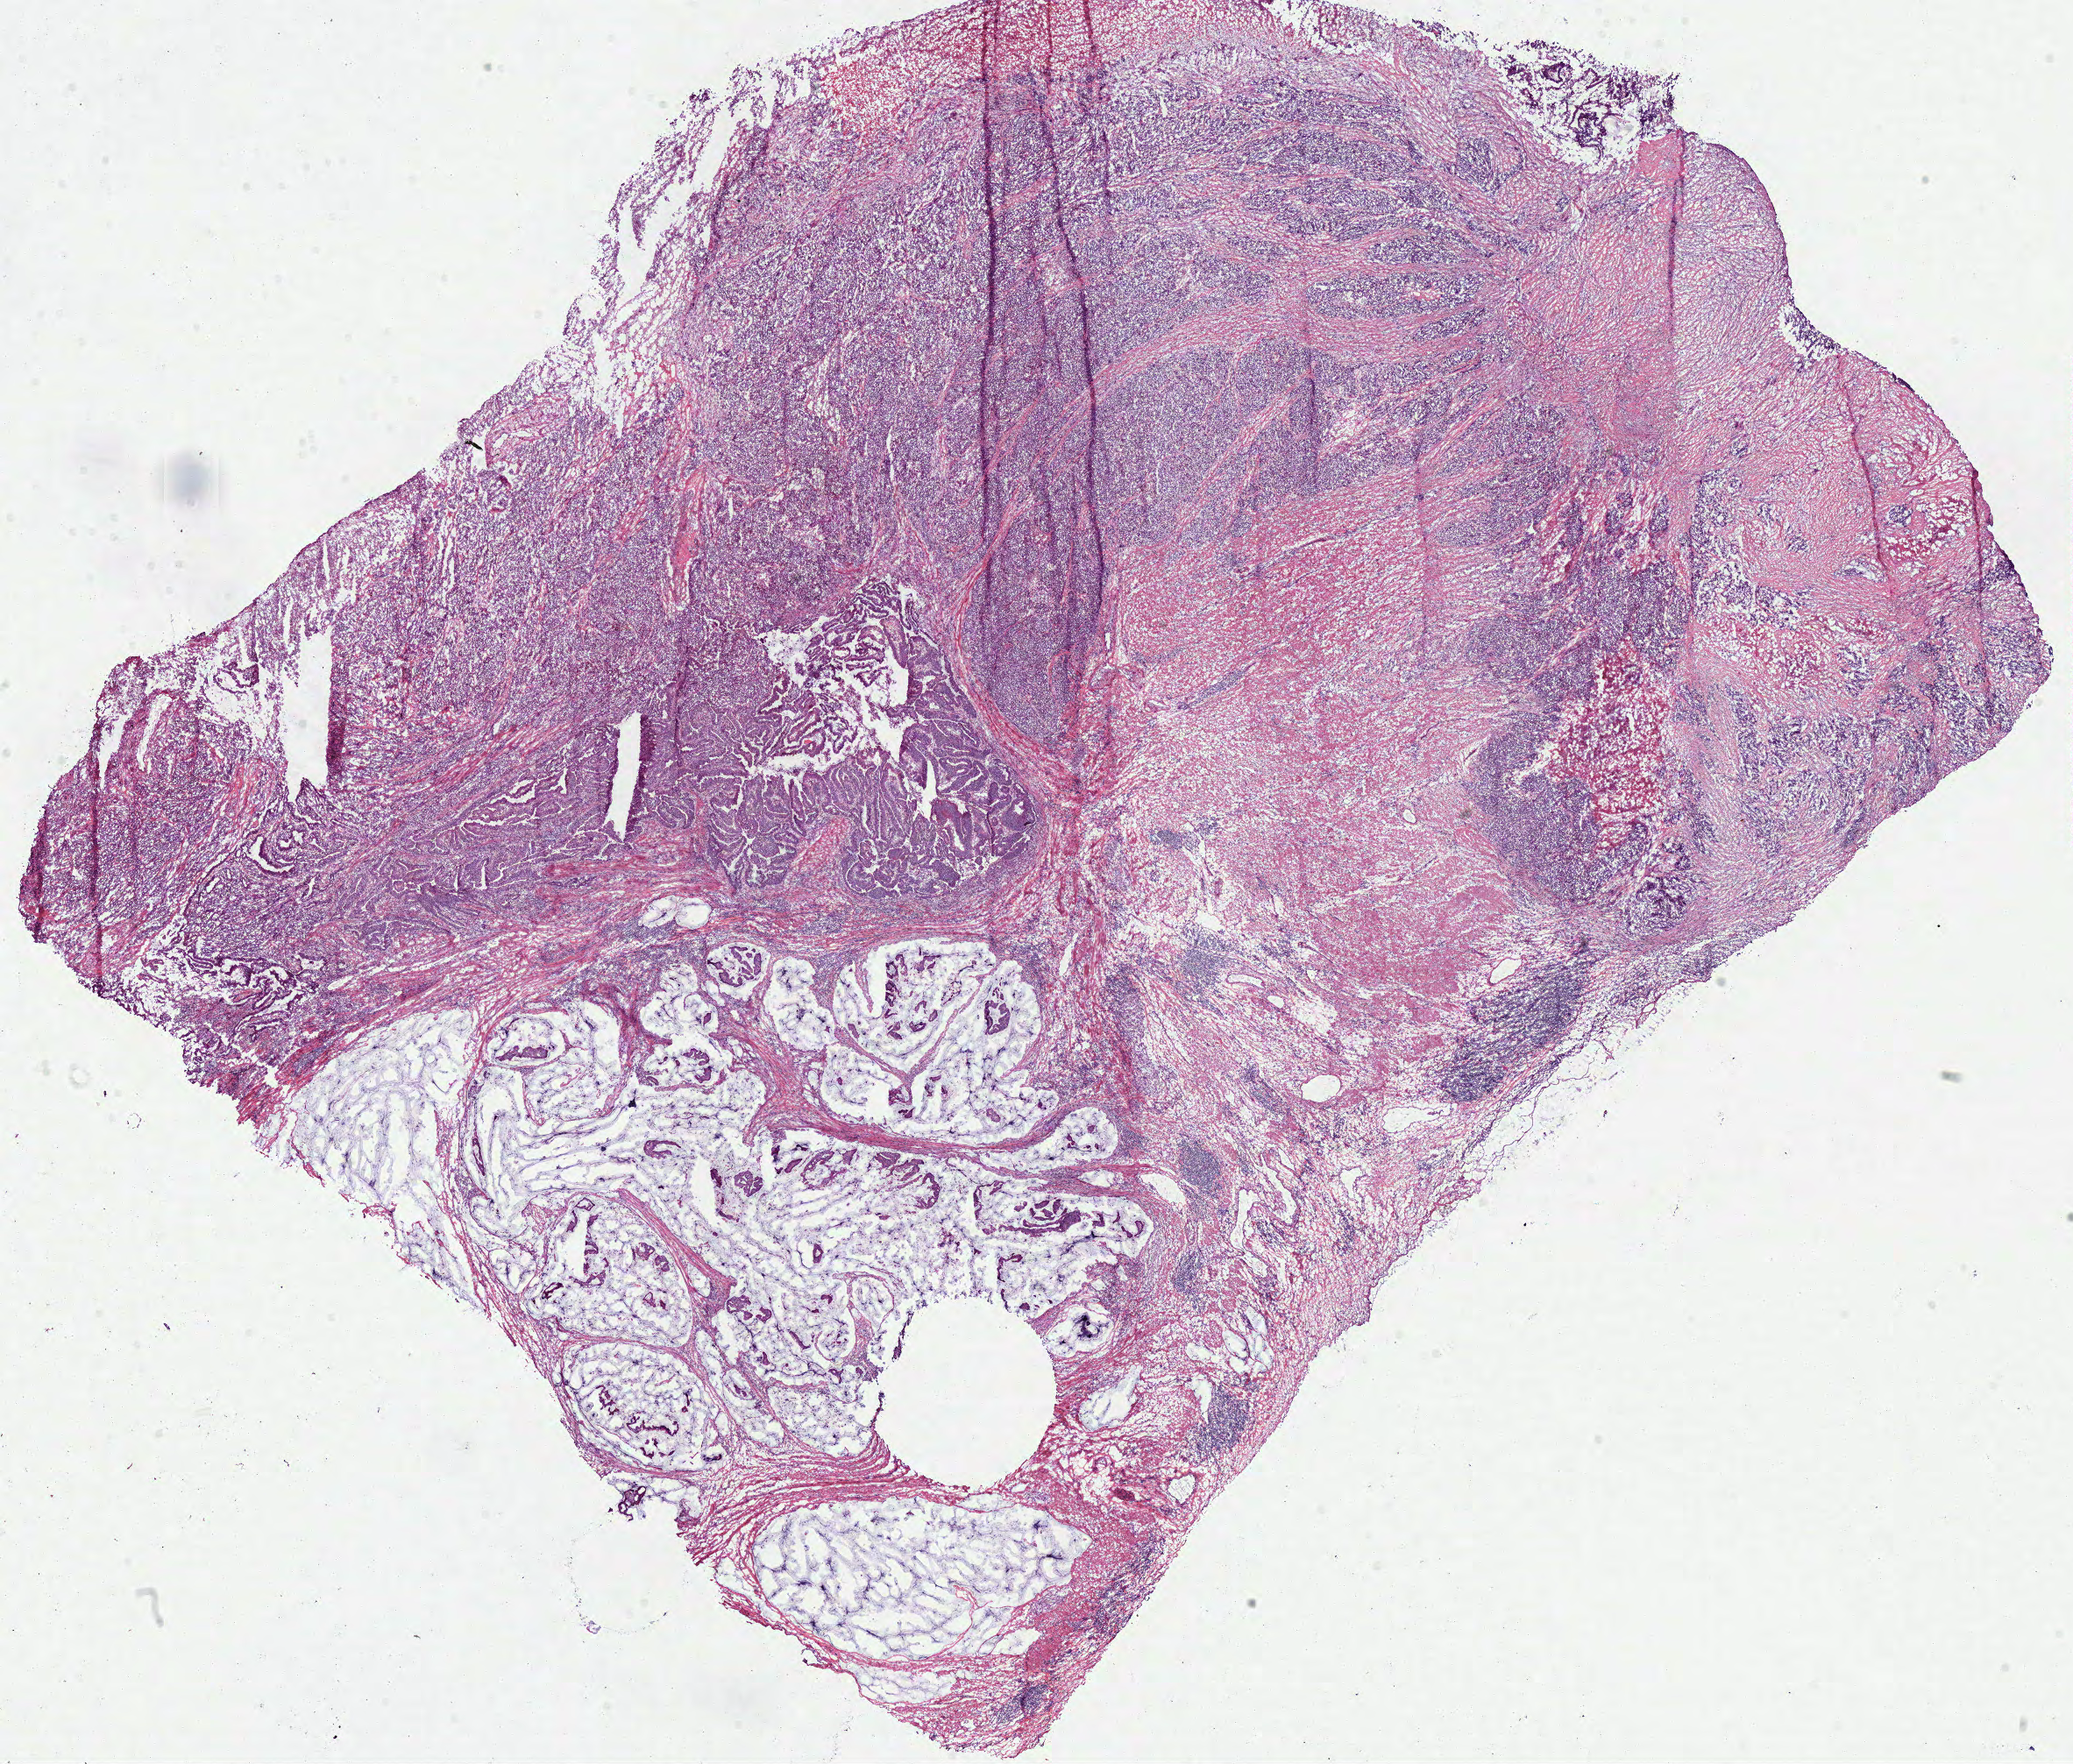
H&E whole-slide image — a low-resolution overview of the entire scanned area, about 18.6 x 15.8 mm (acquisition: 40x scan), frozen section from the bottom of the tissue portion, sample: primary tumour, colon. Male, age 57 years at initial diagnosis. Slide review estimates, as recorded: tumour cells 70%, tumour nuclei 80%, normal cells 0%, stromal cells 25%, necrosis 5%.
Diagnosis: Mucinous adenocarcinoma. AJCC pathologic stage: IIA.